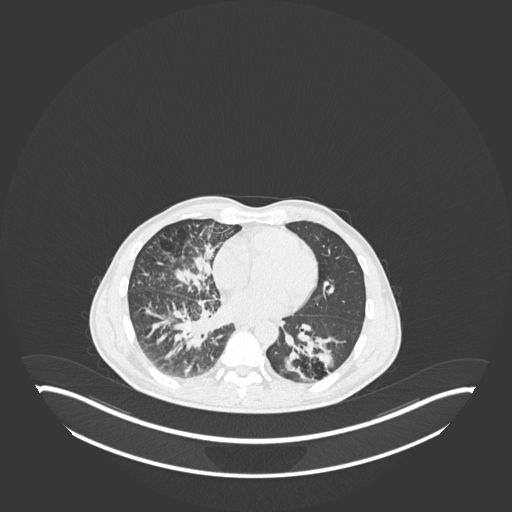
Chest CT, one axial slice; position 98 of 237 along the scan axis; reconstruction kernel B30f; 120 kVp; lung window (W 1500 / L -600 HU); 1 mm slice thickness; 512 × 512 image matrix, field of view 500 × 500 mm. Patient: male, 49 years. From the clinical record (not read from this slice): clinical TNM (as recorded): T2b N1 M0.
Annotated regions visible in this slice (rectangle marked by the reading radiologist):
- lung tumour (recorded histology: adenocarcinoma): bounding box <285,328,337,383> (left, top, right, bottom; pixels)